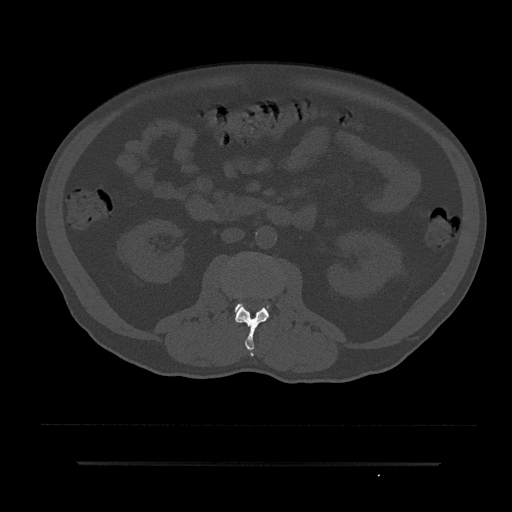
CT including the spine, one axial slice. Slice 46 of 797 in the series (ordered by position). Reconstruction kernel Br40s/3. Bone window (W 1800 / L 400 HU). 0.5 mm slice thickness. 512 × 512 image matrix, field of view 464 × 464 mm. Patient: male, 59 years. From the clinical record (not read from this slice): primary cancer: bile ducts.
Outlined on this slice (semi-automatic segmentation, software-assisted and operator-edited):
- L2 vertebra: bounding box <235,294,269,357> (left, top, right, bottom; pixels)